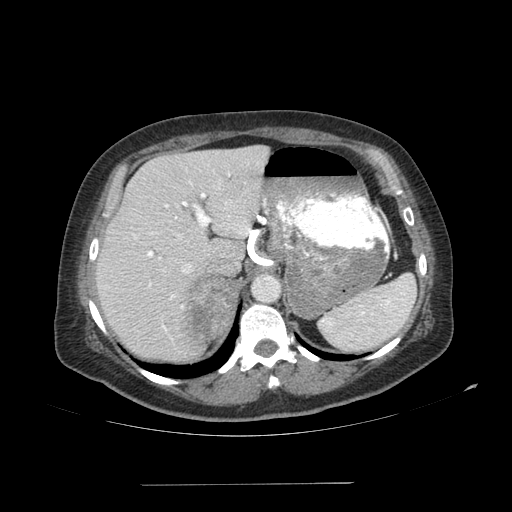
Contrast-enhanced abdominal CT, one axial slice. Slice 77 of 113 in the series (ordered by position). Soft-tissue window (W 400 / L 40 HU). 2.5 mm slice thickness. 512 × 512 image matrix, field of view 440 × 440 mm. Patient: female, 67 years. Case-level facts recorded for this patient, not image findings: diagnosis: adrenocortical carcinoma; tumour side: right adrenal; tumour size at pathology: 9.8 cm; Ki-67 index: 59 %; stage (as recorded): 4.
Annotated regions visible in this slice (semi-automatically segmented with operator editing):
- mass: bounding box <183,275,237,339> (left, top, right, bottom; pixels)